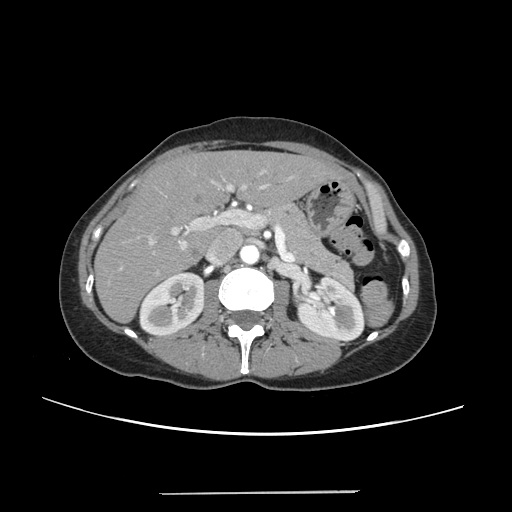
Contrast-enhanced abdominal CT, one axial slice; 120 kVp; intravenous contrast given; soft-tissue window (W 400 / L 40 HU); 1.25 mm slice thickness; 512 × 512 image matrix, field of view 371 × 371 mm. Female patient, age 60 years. Case-level facts recorded for this patient, not image findings: diagnosis: colorectal cancer liver metastases, imaged before liver resection; multiple liver metastases: no; largest metastasis: 1.5 cm; chemotherapy before resection: yes.
Outlined on this slice (expert manual segmentation):
- liver: bounding box [x1, y1, x2, y2] px = [96, 152, 336, 321]
- planned liver remnant (the part of the liver to remain after resection): [96, 152, 335, 321]
- portal vein (with intrahepatic branches): [120, 169, 291, 274]